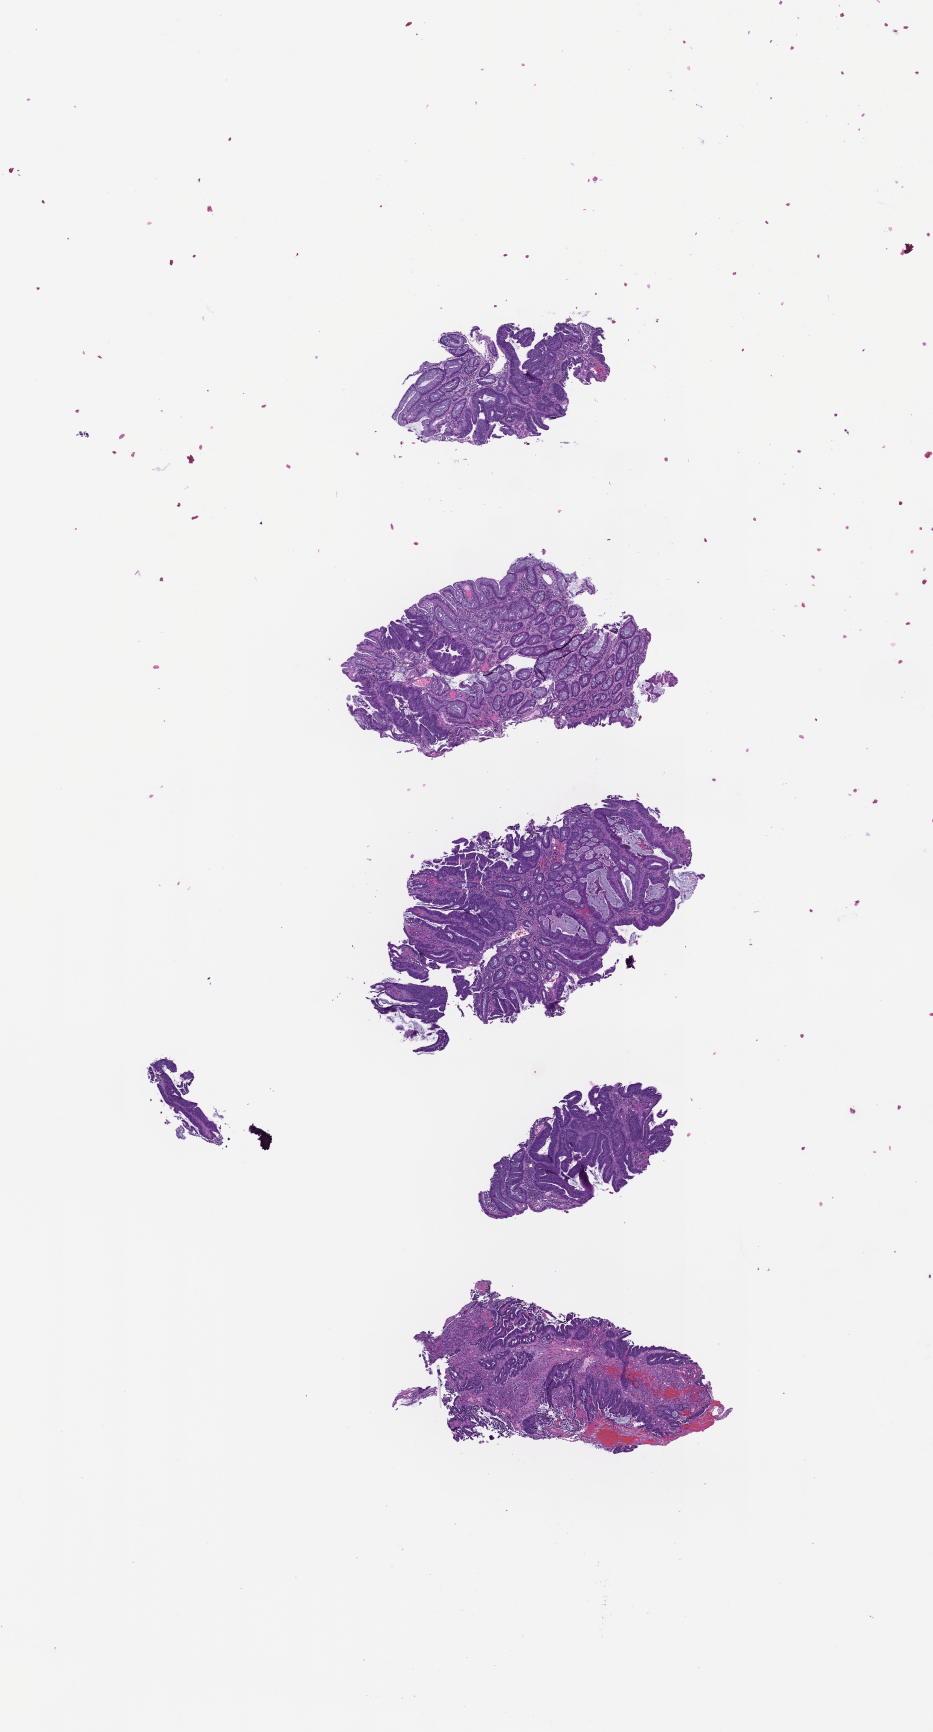
Digitized hematoxylin and eosin (H&E)-stained section, shown as a low-resolution overview of the whole scanned area (about 7.5 x 14.0 mm). Formalin-fixed, paraffin-embedded (FFPE) tissue. Tissue site: colon. Patient sex: male.
This section: primary tumor. Diagnosis: Colorectal Carcinoma.